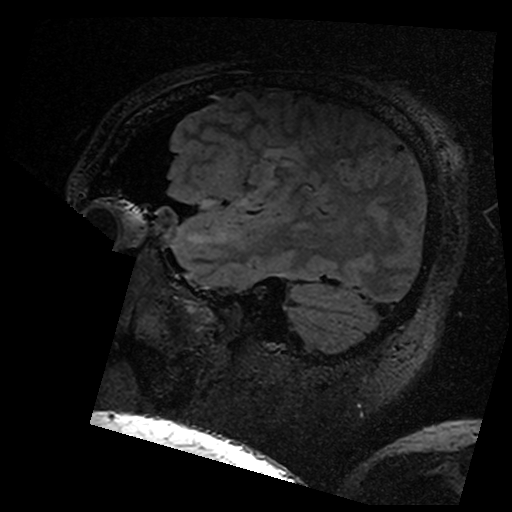
Brain MRI from a brain-tumour surgery series, one sagittal slice. Slice 131 of 176 in the series (ordered by position). T2 FLAIR. 512 × 512 image matrix, field of view 250 × 250 mm. From the clinical record (not read from this slice): histopathology: Astrocytoma; WHO grade: 3; IDH mutation: yes; tumour location: Left Insular.
Outlined on this slice (outlined manually by an expert reader):
- residual tumour: box from (x=277, y=154) to (x=291, y=165) px